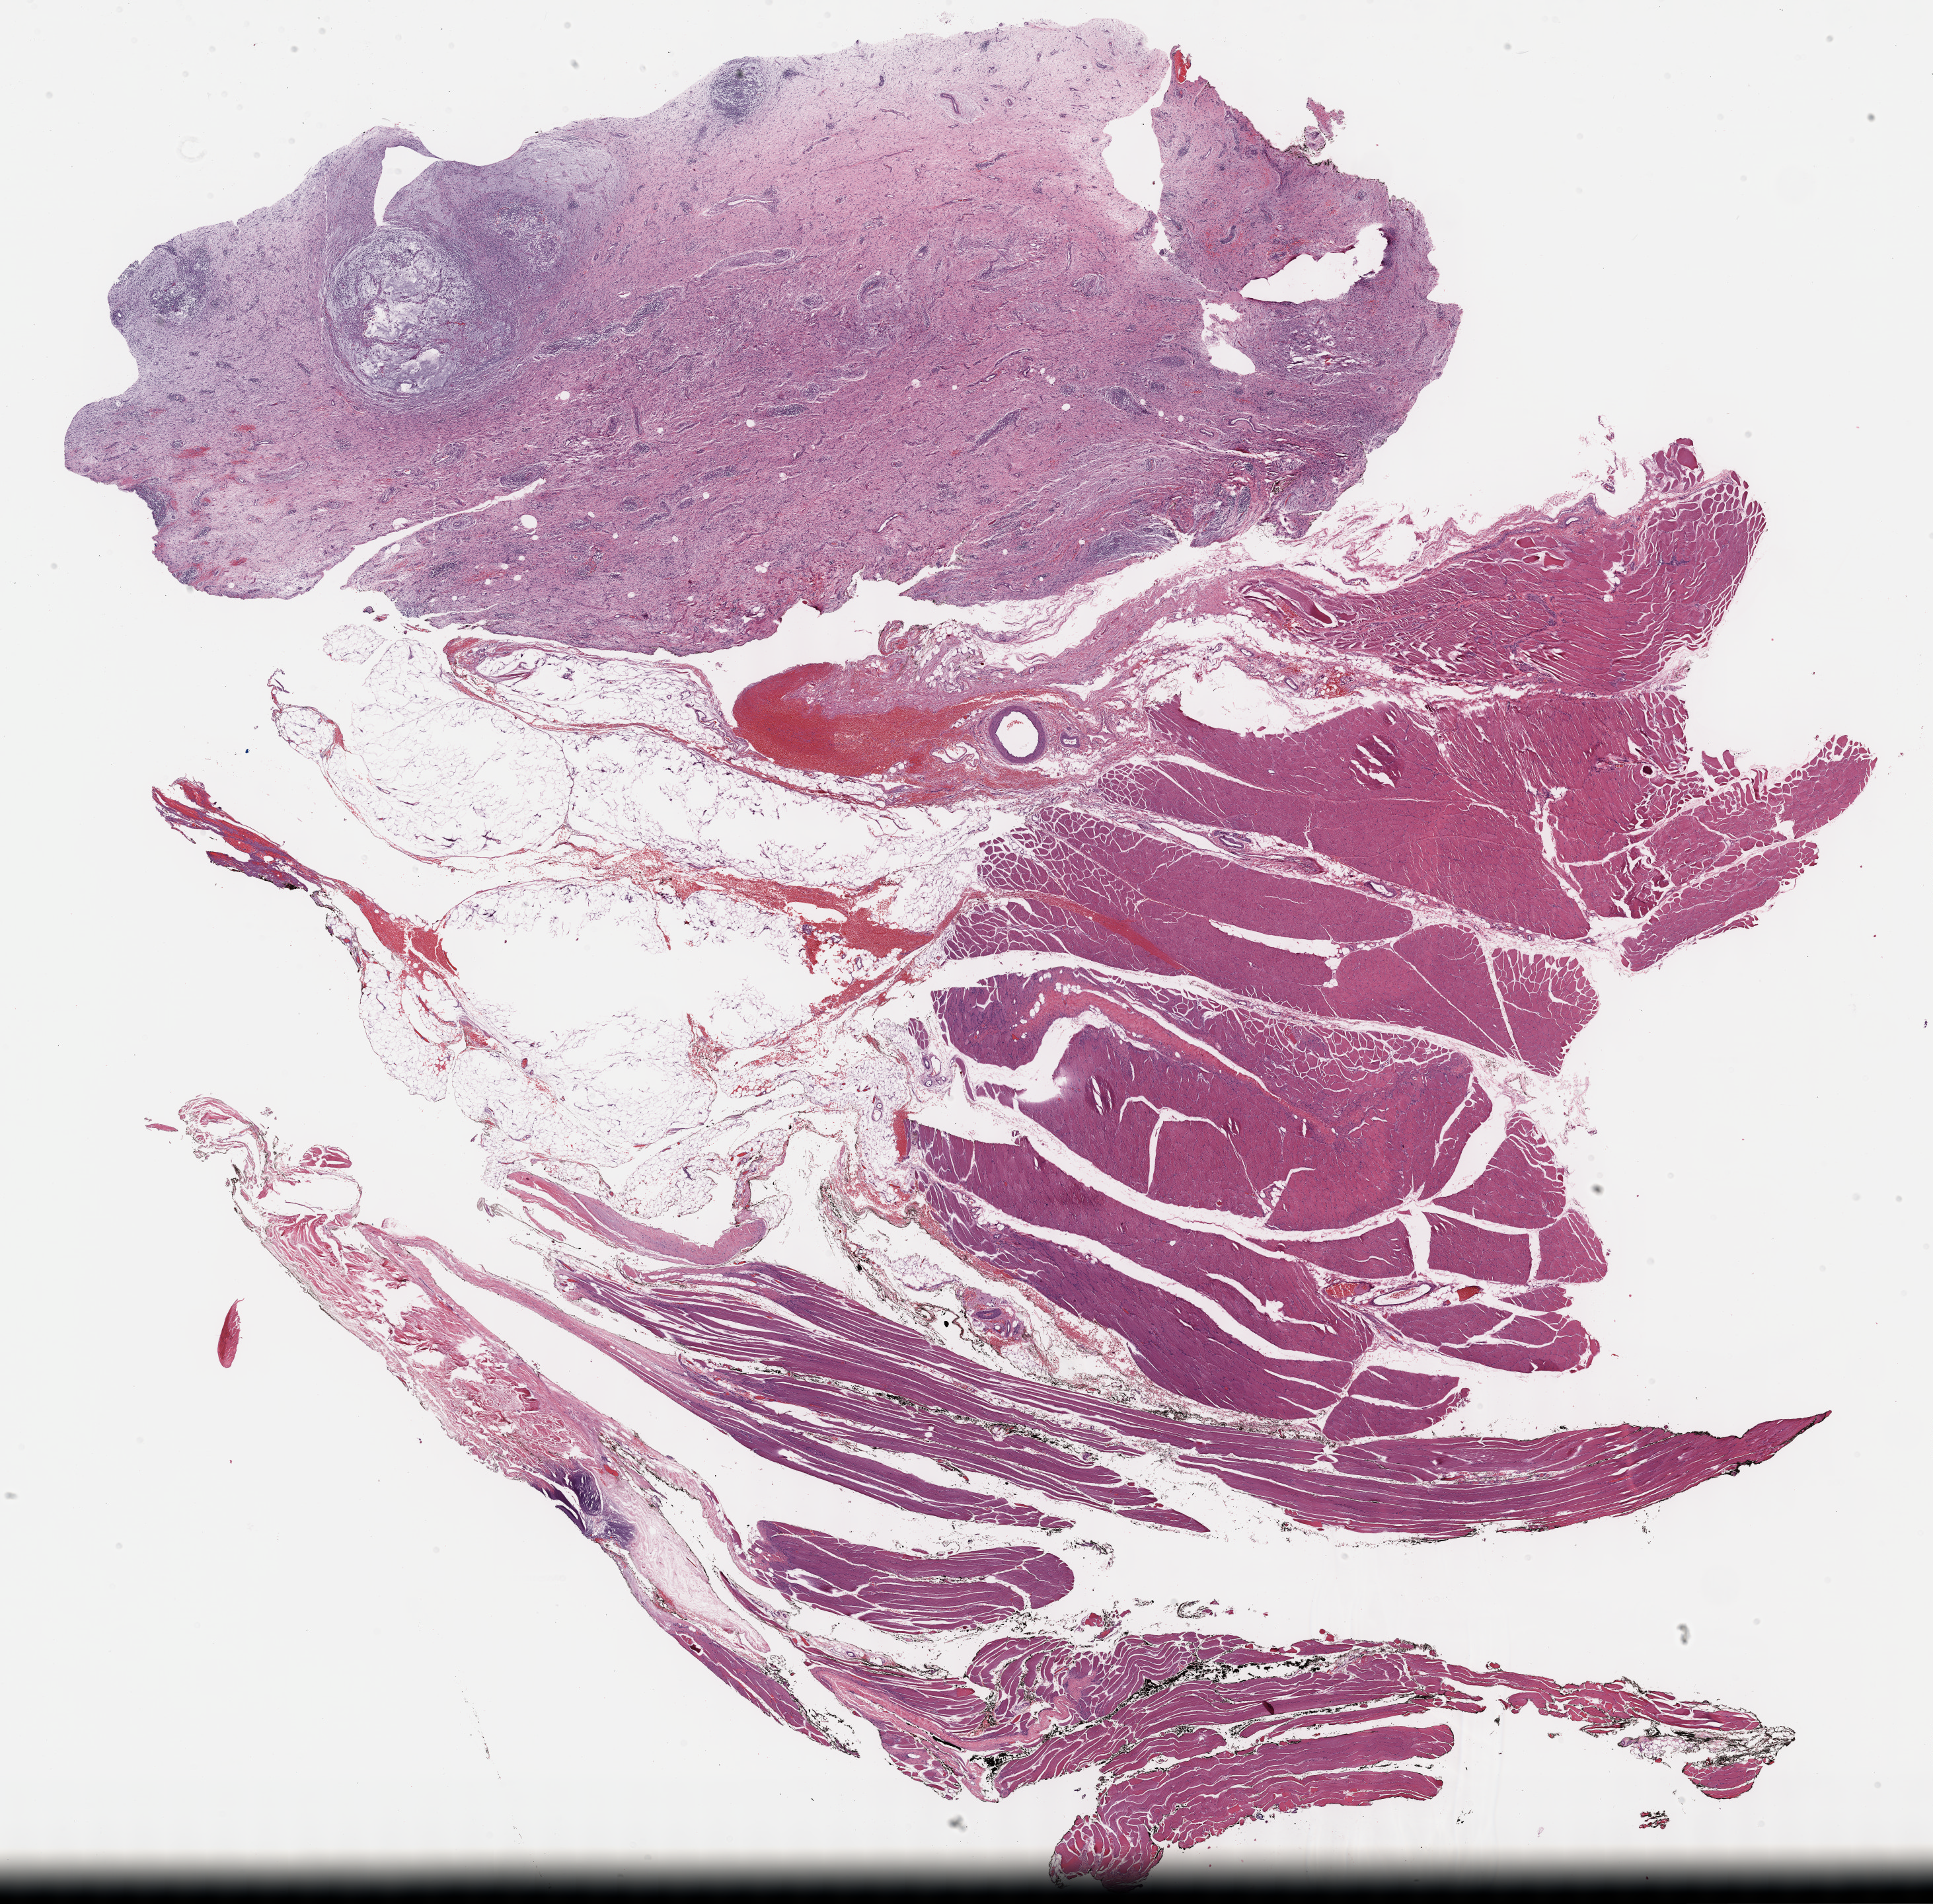
Whole-slide histology image, H&E-stained, low-resolution overview of the scanned area, about 23.7 x 23.3 mm (from a 40x scan), formalin-fixed paraffin-embedded (FFPE) diagnostic section, sample: primary tumour, connective, subcutaneous and other soft tissues. Patient: female, age at initial diagnosis 53 years.
• histologic diagnosis: Fibromyxosarcoma (connective, subcutaneous and other soft tissues of trunk, NOS)